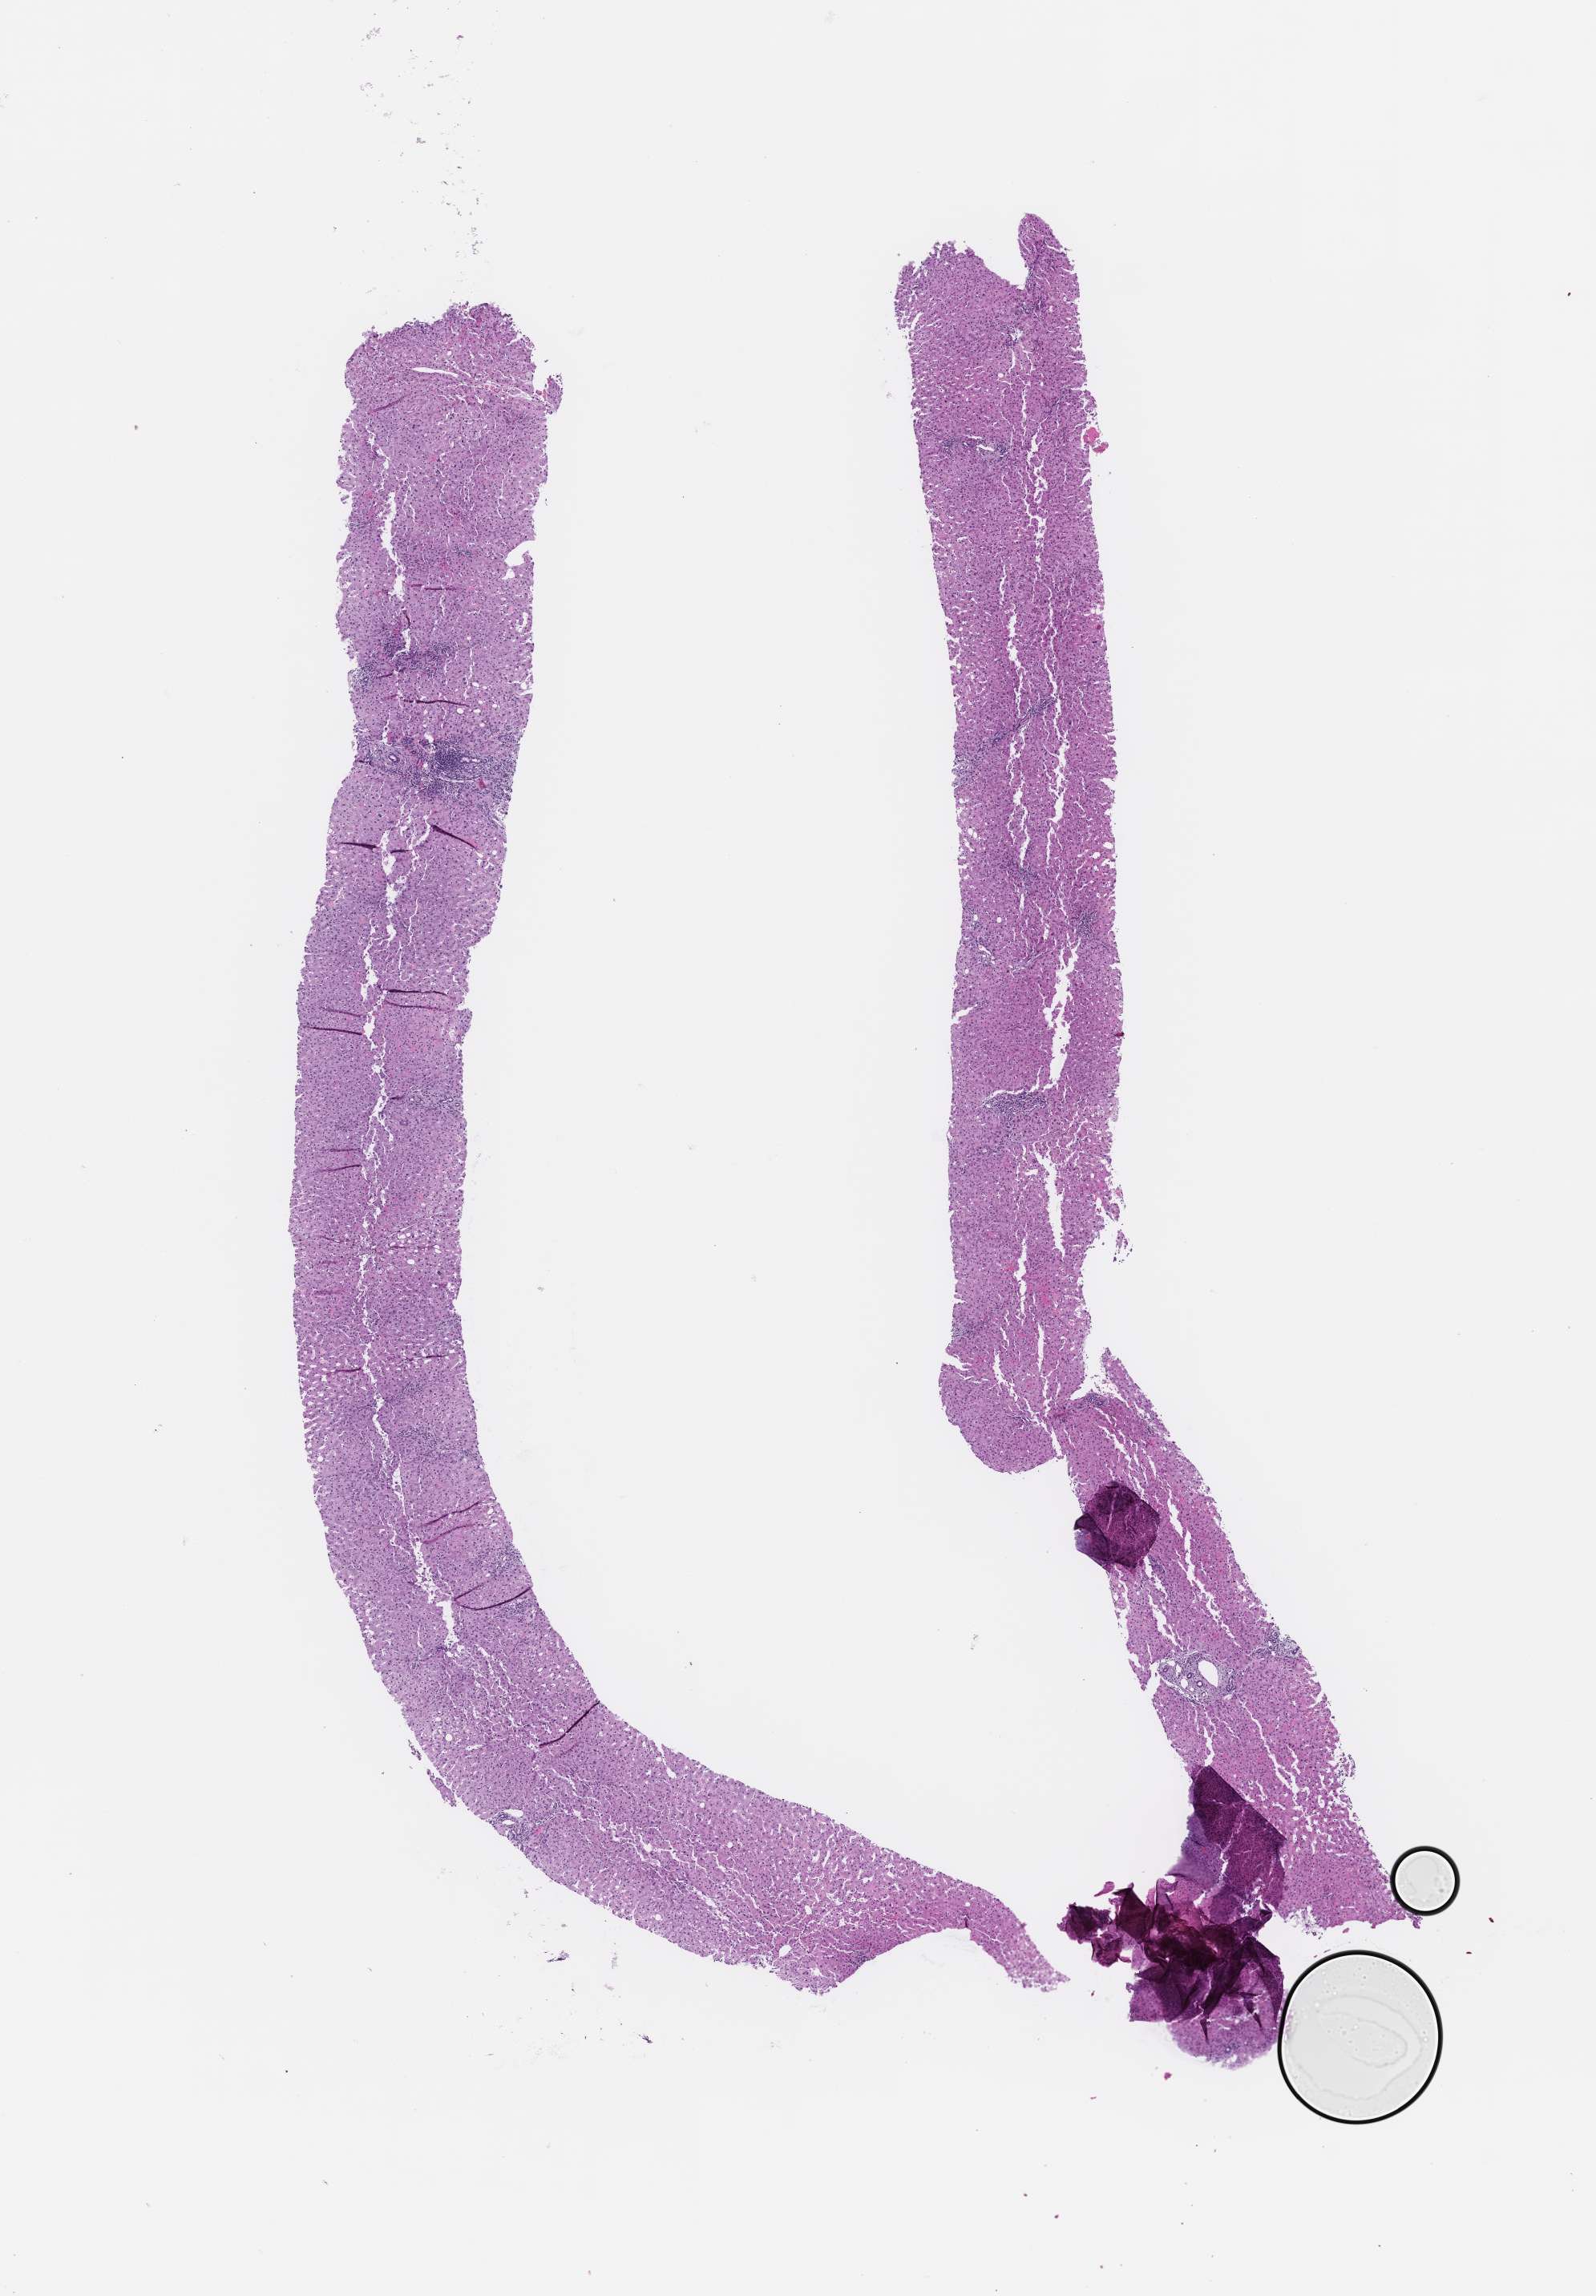
Haematoxylin and eosin whole-slide image, low-resolution overview of the scanned area, about 8.0 x 11.6 mm, formalin-fixed, paraffin-embedded (FFPE) tissue, collected at baseline (before treatment). Patient: male.
This section: metastasis (sampled organ not recorded). Patient diagnosis (primary): Colorectal Carcinoma.